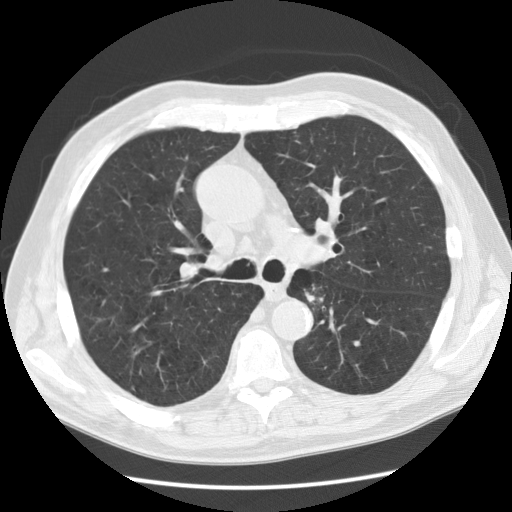
Axial slice from a low-dose chest CT screening exam. Second screening round (one year after baseline). Lung window (W 1500 / L -600 HU). 120 kVp. Slice 48 of 130 in the series. 512 × 512 image matrix. Male, age 73 years at enrolment.
• Expert-annotated lung lesion, bounding box [x1, y1, x2, y2] px = [292, 274, 339, 318].
• The screening reader recorded 4 non-calcified nodules or masses ≥4 mm on this exam; which of them this box marks is not recorded.
• Lung cancer was diagnosed 302 days after this screen: small cell carcinoma, NOS, left lower lobe, stage IIIB (AJCC 6th edition), 55 mm at pathology.